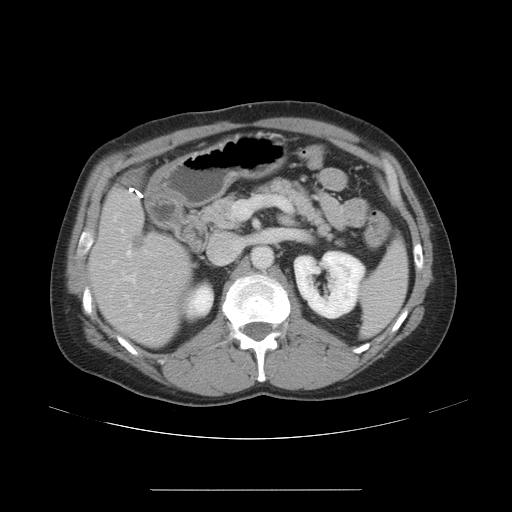
Contrast-enhanced abdominal CT, one axial slice. Position 24 of 48 along the scan axis. Reconstruction kernel STANDARD. Intravenous contrast given. Soft-tissue window (W 400 / L 40 HU). 5 mm slice thickness. 512 × 512 image matrix. Male patient, age 56 years. From the clinical record (not read from this slice): diagnosis: colorectal cancer liver metastases, imaged before liver resection; multiple liver metastases: yes; largest metastasis: 1.8 cm; disease in both lobes: yes.
Annotated regions visible in this slice (manually delineated by an expert):
- hepatic veins: bounding box <112,245,154,319> (left, top, right, bottom; pixels)
- liver: <90,188,191,347>
- planned liver remnant (the part of the liver to remain after resection): <93,188,191,347>
- portal vein (with intrahepatic branches): <120,228,136,283>
- liver metastasis: <133,238,144,250>